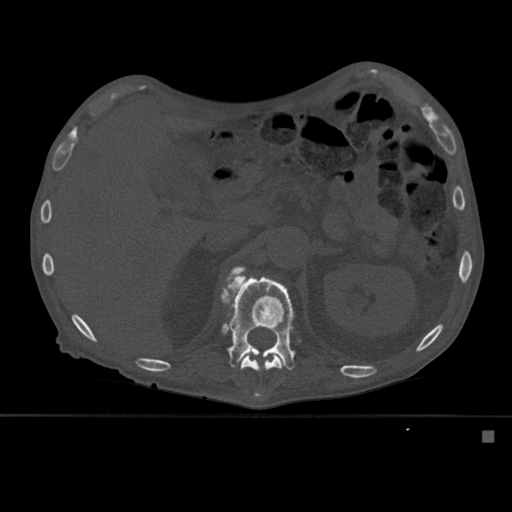
CT including the spine, one axial slice. Position 263 of 527 along the scan axis. Bone window (W 1800 / L 400 HU). 1.5 mm slice thickness. 512 × 512 image matrix, field of view 373 × 373 mm. Male patient, age 78 years. Case-level facts recorded for this patient, not image findings: primary cancer: prostate.
Structures marked on this image (semi-automatically segmented with operator editing):
- L1 vertebra: bounding box [x1, y1, x2, y2] px = [220, 273, 296, 398]
- T12 vertebra: [230, 265, 282, 396]